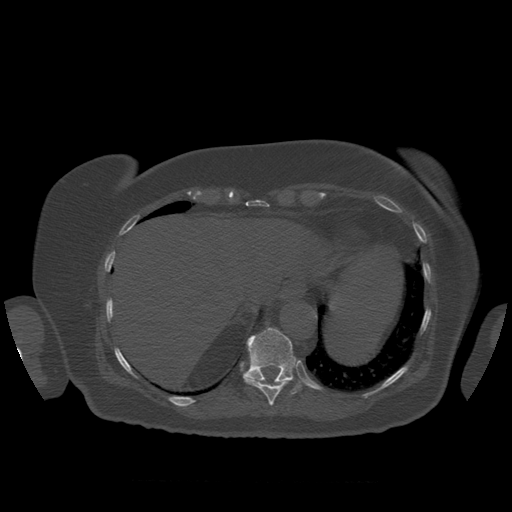
CT including the spine, one axial slice. Position 331 of 399 along the scan axis. Bone window (W 1800 / L 400 HU). 1.25 mm slice thickness. 512 × 512 image matrix, field of view 404 × 404 mm. Patient age 81 years. Case-level facts recorded for this patient, not image findings: primary cancer: renal.
Structures marked on this image (semi-automatic segmentation, software-assisted and operator-edited):
- T10 vertebra: box from (x=244, y=376) to (x=293, y=406) px
- T11 vertebra: (x=244, y=328)–(x=301, y=395)